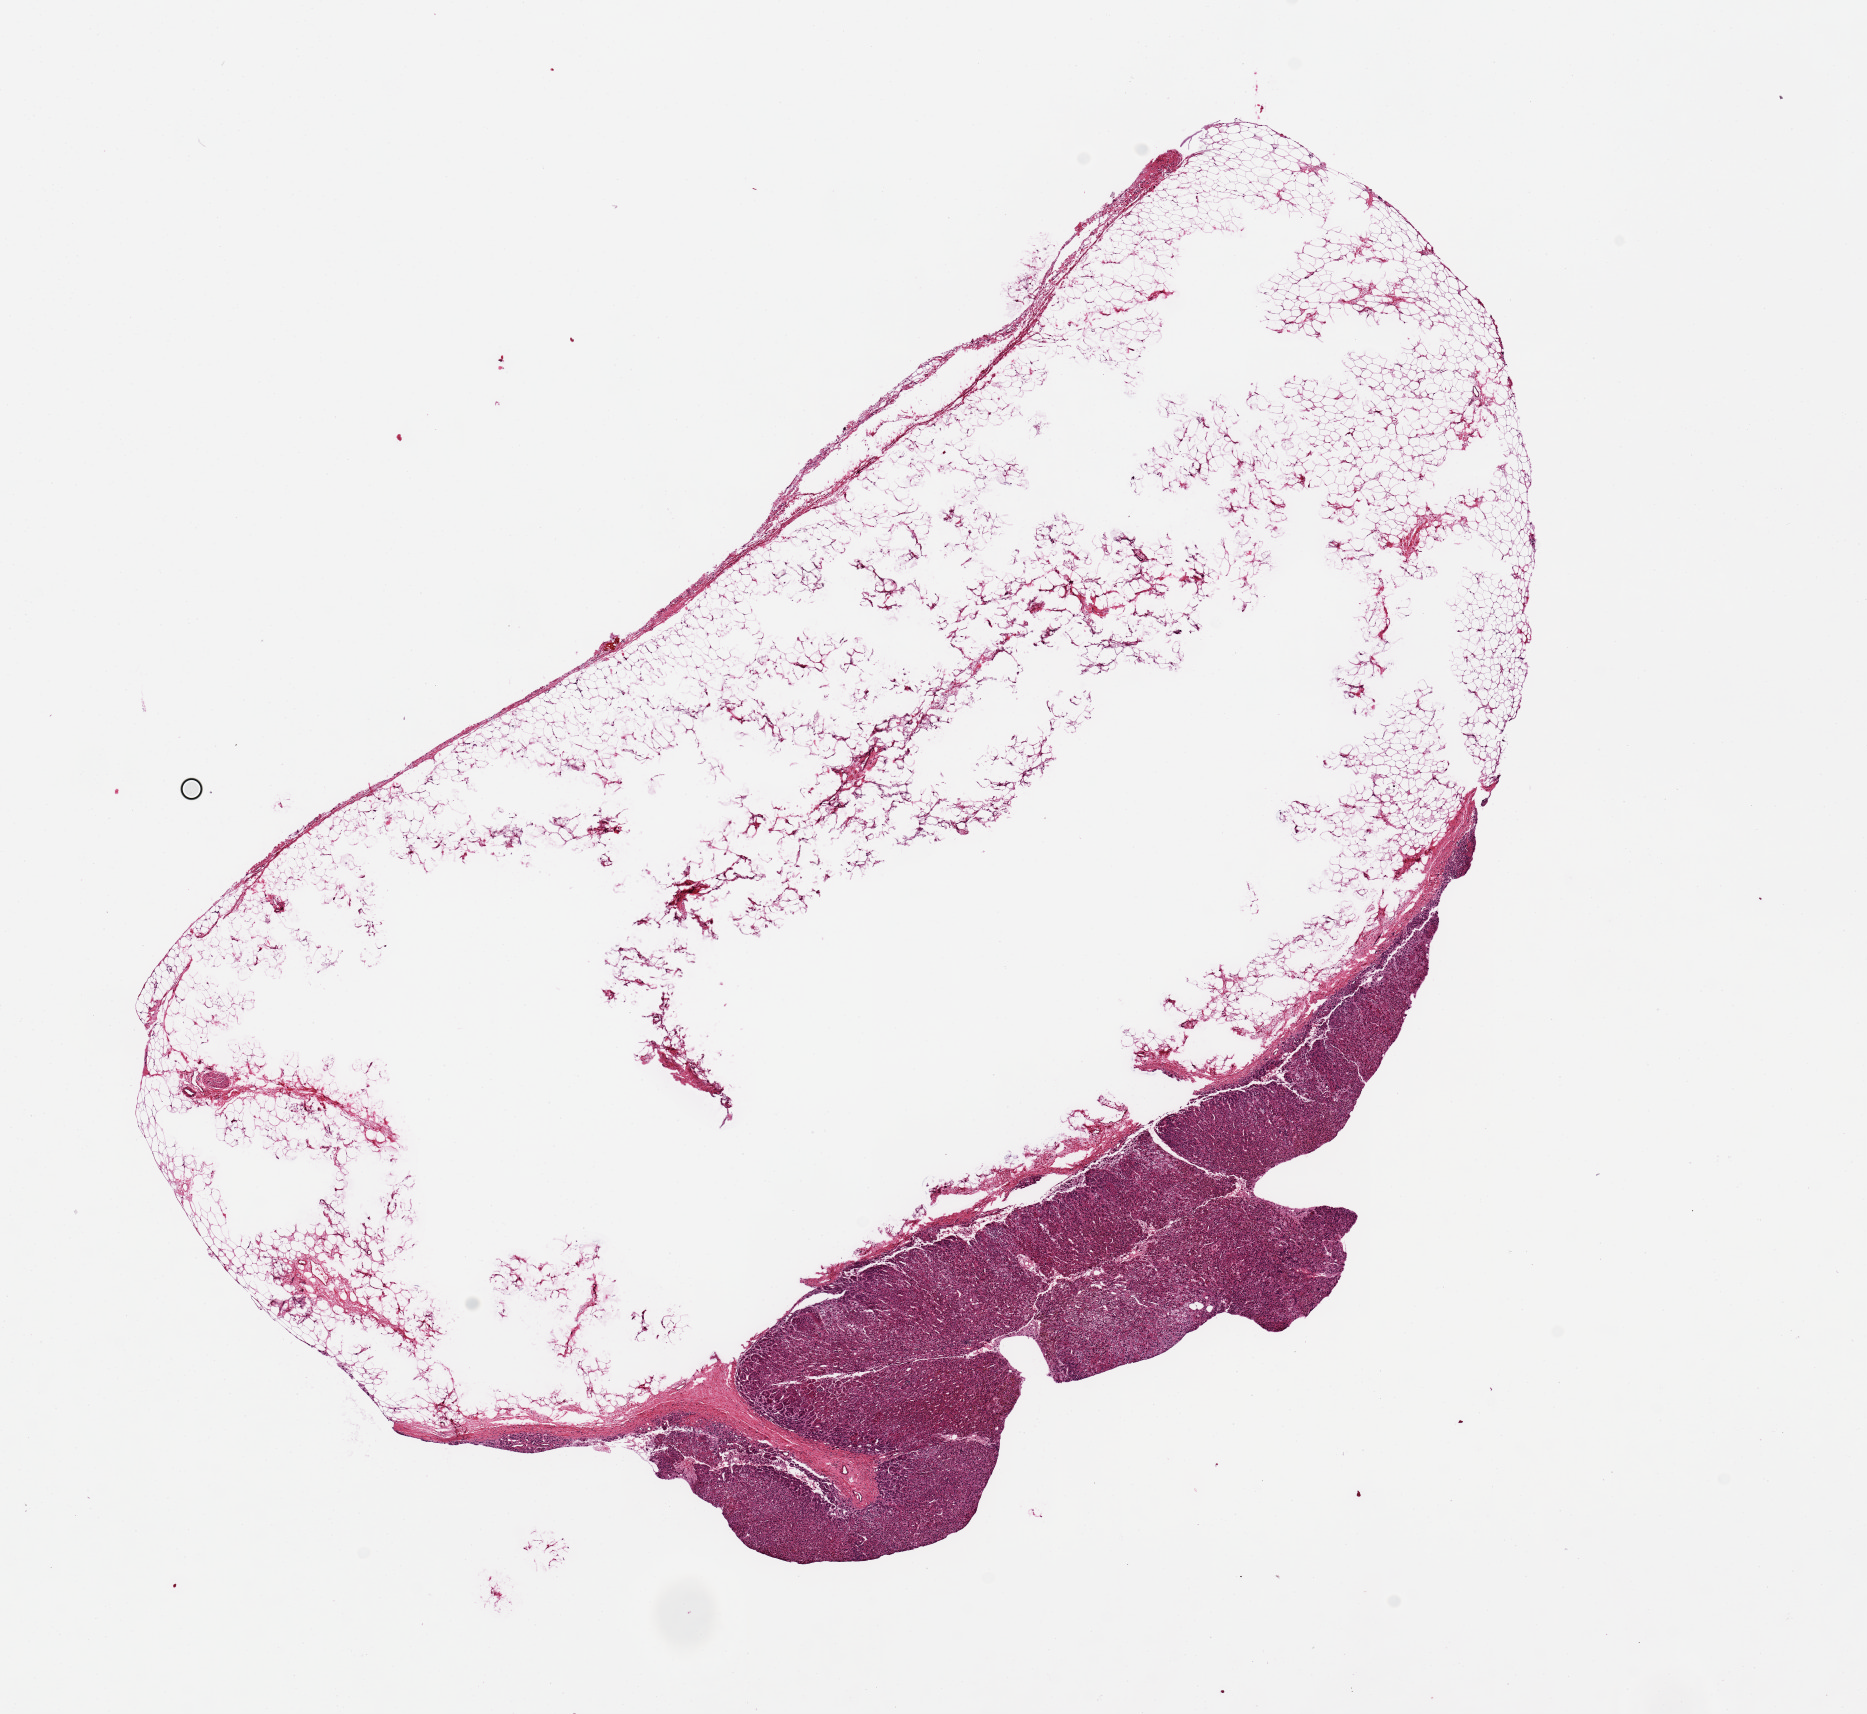
H&E whole-slide image, a low-resolution overview of the entire scanned area, about 14.8 x 13.6 mm, PAXgene-fixed, paraffin-embedded tissue, sampled site (target tissue): adrenal gland, donor tissue sample. Donor sex: male.
Pathologist's review note for this sample: Well preserved. 1.3 x 6mm nubbin of cortex attached to a 12 x 7mm fat globule, roughly 10% of specimen. Fat is under-fixed centrally.